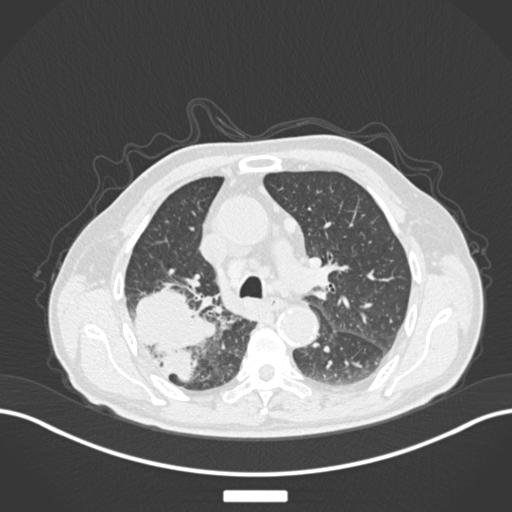
Chest CT, one axial slice. Position 121 of 201 along the scan axis. Reconstruction kernel B30f. Lung window (W 1500 / L -600 HU). 1 mm slice thickness. 512 × 512 image matrix, field of view 400 × 400 mm. Male patient, age 72 years. From the clinical record (not read from this slice): clinical TNM (as recorded): T3 N2 M0.
Structures marked on this image (rectangle marked by the reading radiologist):
- lung tumour (recorded histology: adenocarcinoma): bounding box (x1, y1, x2, y2) in pixels: (131, 281, 219, 386)